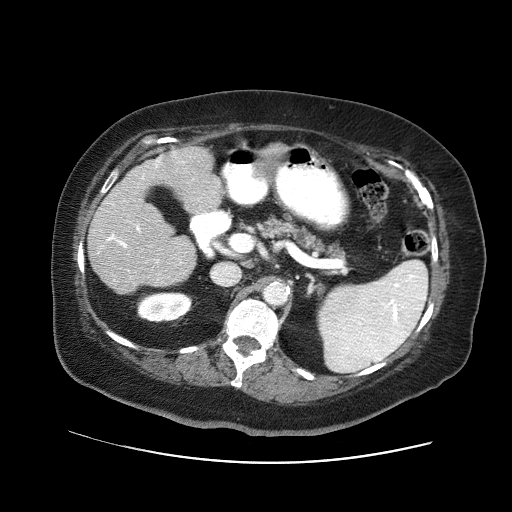
Contrast-enhanced abdominal CT (liver protocol), one axial slice; slice 21 of 71 in the series (ordered by position); reconstruction kernel STANDARD; 120 kVp; soft-tissue window (W 400 / L 40 HU); 512 × 512 image matrix. From the clinical record (not read from this slice): diagnosis: hepatocellular carcinoma (patient treated with transarterial chemoembolisation; whether this scan precedes or follows treatment is not stated here); TNM stage (as recorded): Stage-II; Child-Pugh class: A; tumour size: 5 cm.
Annotated regions visible in this slice (semi-automatic segmentation, software-assisted and operator-edited):
- liver parenchyma outside the tumour (the mass and vessels are separate outlines, so this box may not span the whole liver): bounding box <88,144,286,292> (left, top, right, bottom; pixels)
- liver vessels: <107,152,176,262>